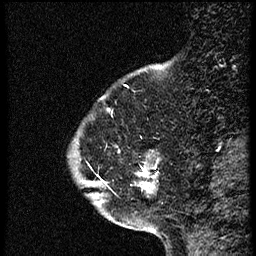
Breast MRI (dynamic contrast-enhanced), one sagittal slice. Position 9 of 56 along the scan axis. Dynamic contrast-enhanced study with each time point stored as its own series, time point 2 of 4 at this slice position (early post-contrast, ordered by acquisition time). 1.5 T. TE 4.2 ms, TR 18.9 ms. 256 × 256 image matrix, field of view 200 × 200 mm. Female patient. Case-level facts recorded for this patient, not image findings: setting: breast cancer imaged before/during neoadjuvant chemotherapy; receptor status: HER2-positive.
Annotated regions visible in this slice (semi-automatic segmentation, software-assisted and operator-edited):
- analysis volume of interest (the breast-tissue region the enhancement analysis was run in; not a lesion): bounding box <69,112,161,215> (left, top, right, bottom; pixels)
- tumour enhancement mask (voxels above the 100 % enhancement threshold inside the analysis volume of interest): <106,174,148,189>